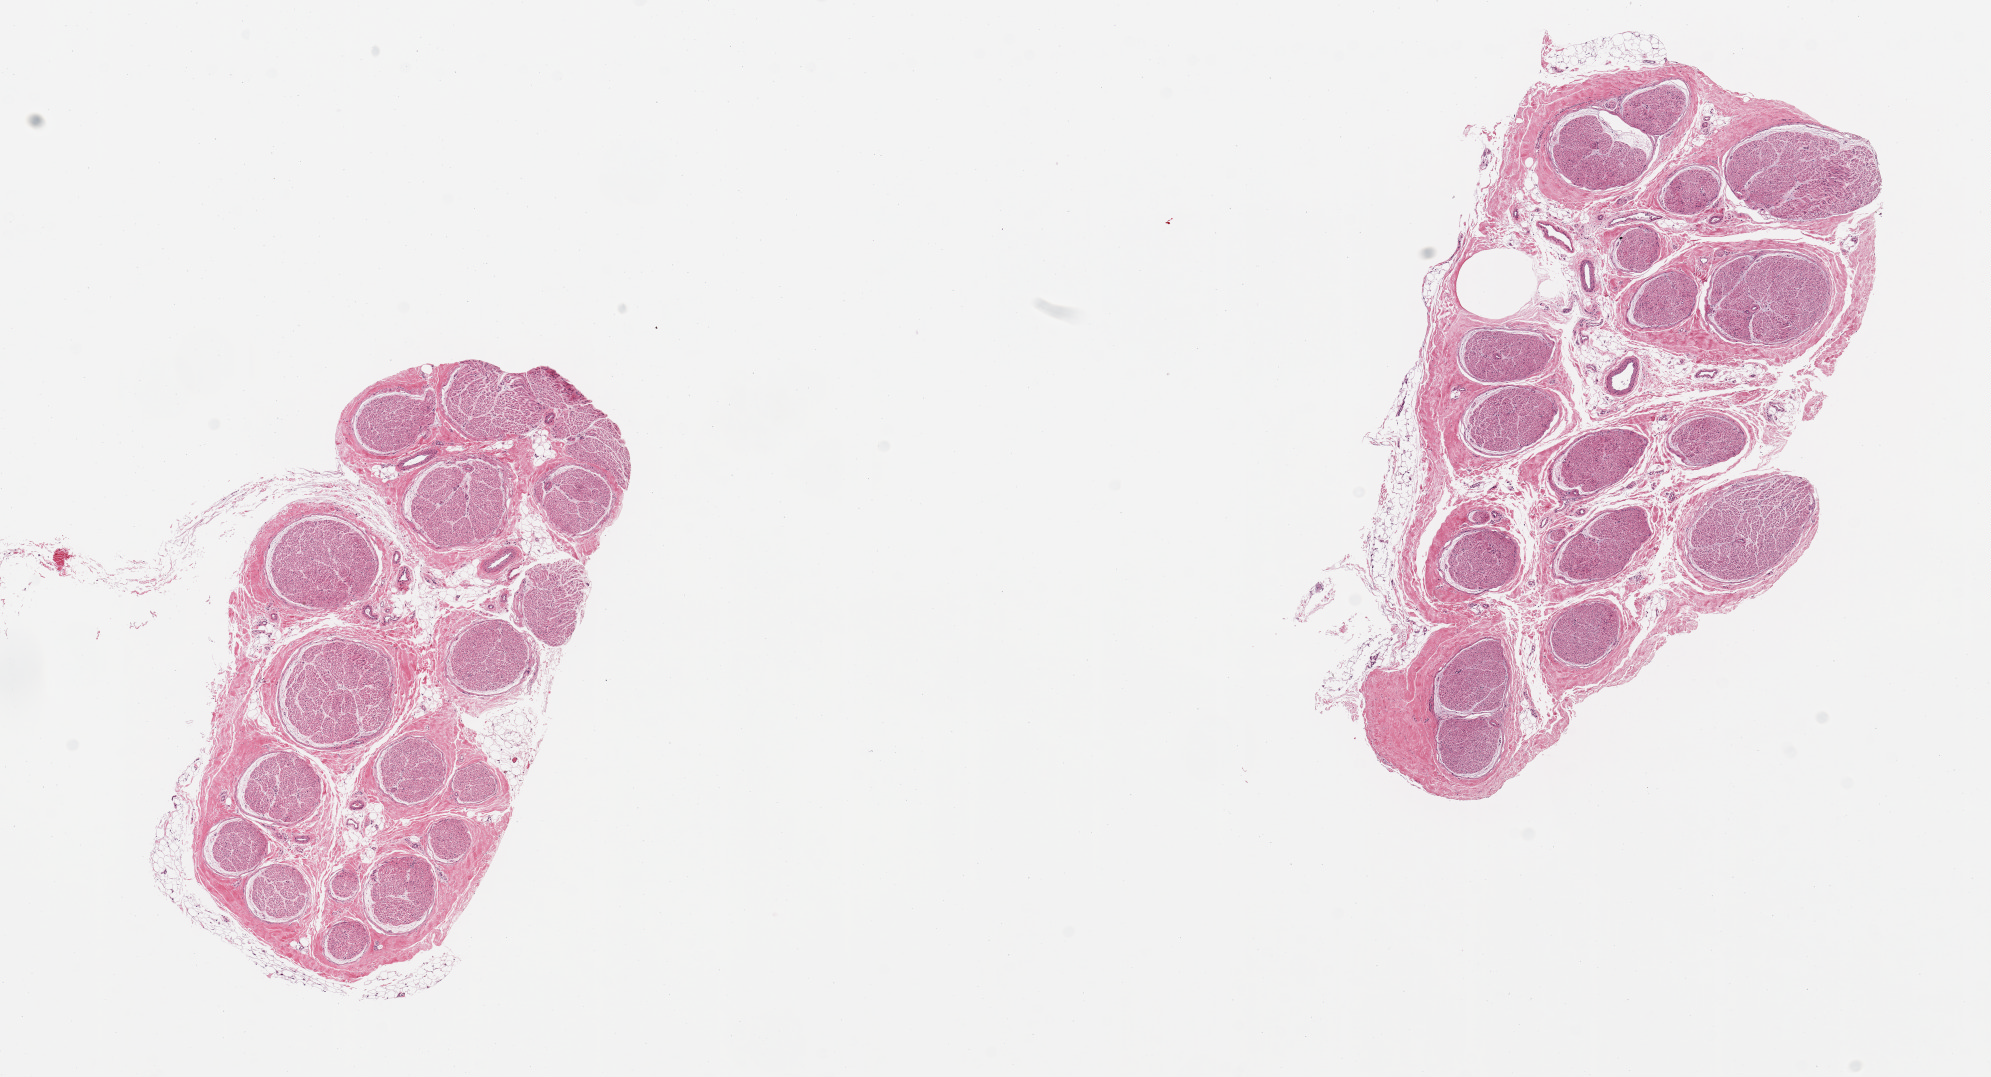
Haematoxylin and eosin whole-slide image — a low-resolution overview of the entire scanned area, about 15.8 x 8.5 mm (acquisition: 20x scan); PAXgene-fixed paraffin-embedded (PFPE) section; target tissue: tibial nerve; donor tissue sample. Donor: male.
- reviewer comment on this tissue sample: 2 pieces, trace adherent fat, ~0.3mm